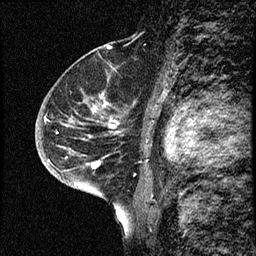
Breast MRI (dynamic contrast-enhanced), one sagittal slice. Slice 46 of 68 in the series (ordered by position). Dynamic contrast-enhanced study with each time point stored as its own series, time point 2 of 3 at this slice position (early post-contrast, ordered by acquisition time). 1.5 T. TE 4.2 ms, TR 17.6 ms. 256 × 256 image matrix, field of view 200 × 200 mm. Patient: female, 52 years. Case-level facts recorded for this patient, not image findings: setting: breast cancer imaged before/during neoadjuvant chemotherapy; receptor status: HER2-positive.
Outlined on this slice (semi-automatic segmentation, software-assisted and operator-edited):
- analysis volume of interest (the breast-tissue region the enhancement analysis was run in; not a lesion): box from (x=50, y=61) to (x=140, y=184) px
- tumour enhancement mask (voxels above the 100 % enhancement threshold inside the analysis volume of interest): (x=93, y=109)–(x=100, y=168)